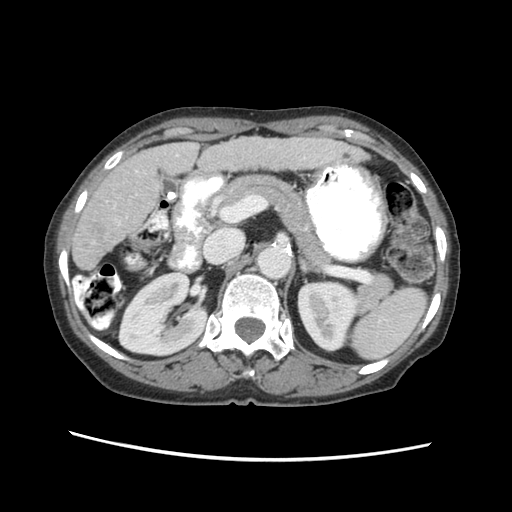
Contrast-enhanced abdominal CT (liver protocol), one axial slice. Position 25 of 63 along the scan axis. Reconstruction kernel STANDARD. 120 kVp. Soft-tissue window (W 400 / L 40 HU). 512 × 512 image matrix. From the clinical record (not read from this slice): diagnosis: hepatocellular carcinoma (patient treated with transarterial chemoembolisation; whether this scan precedes or follows treatment is not stated here); TNM stage (as recorded): Stage-I; Child-Pugh class: B; tumour nodularity: uninodular.
Outlined on this slice (semi-automatically segmented with operator editing):
- liver parenchyma outside the tumour (the mass and vessels are separate outlines, so this box may not span the whole liver): box from (x=72, y=132) to (x=368, y=268) px
- liver vessels: (x=134, y=152)–(x=175, y=170)